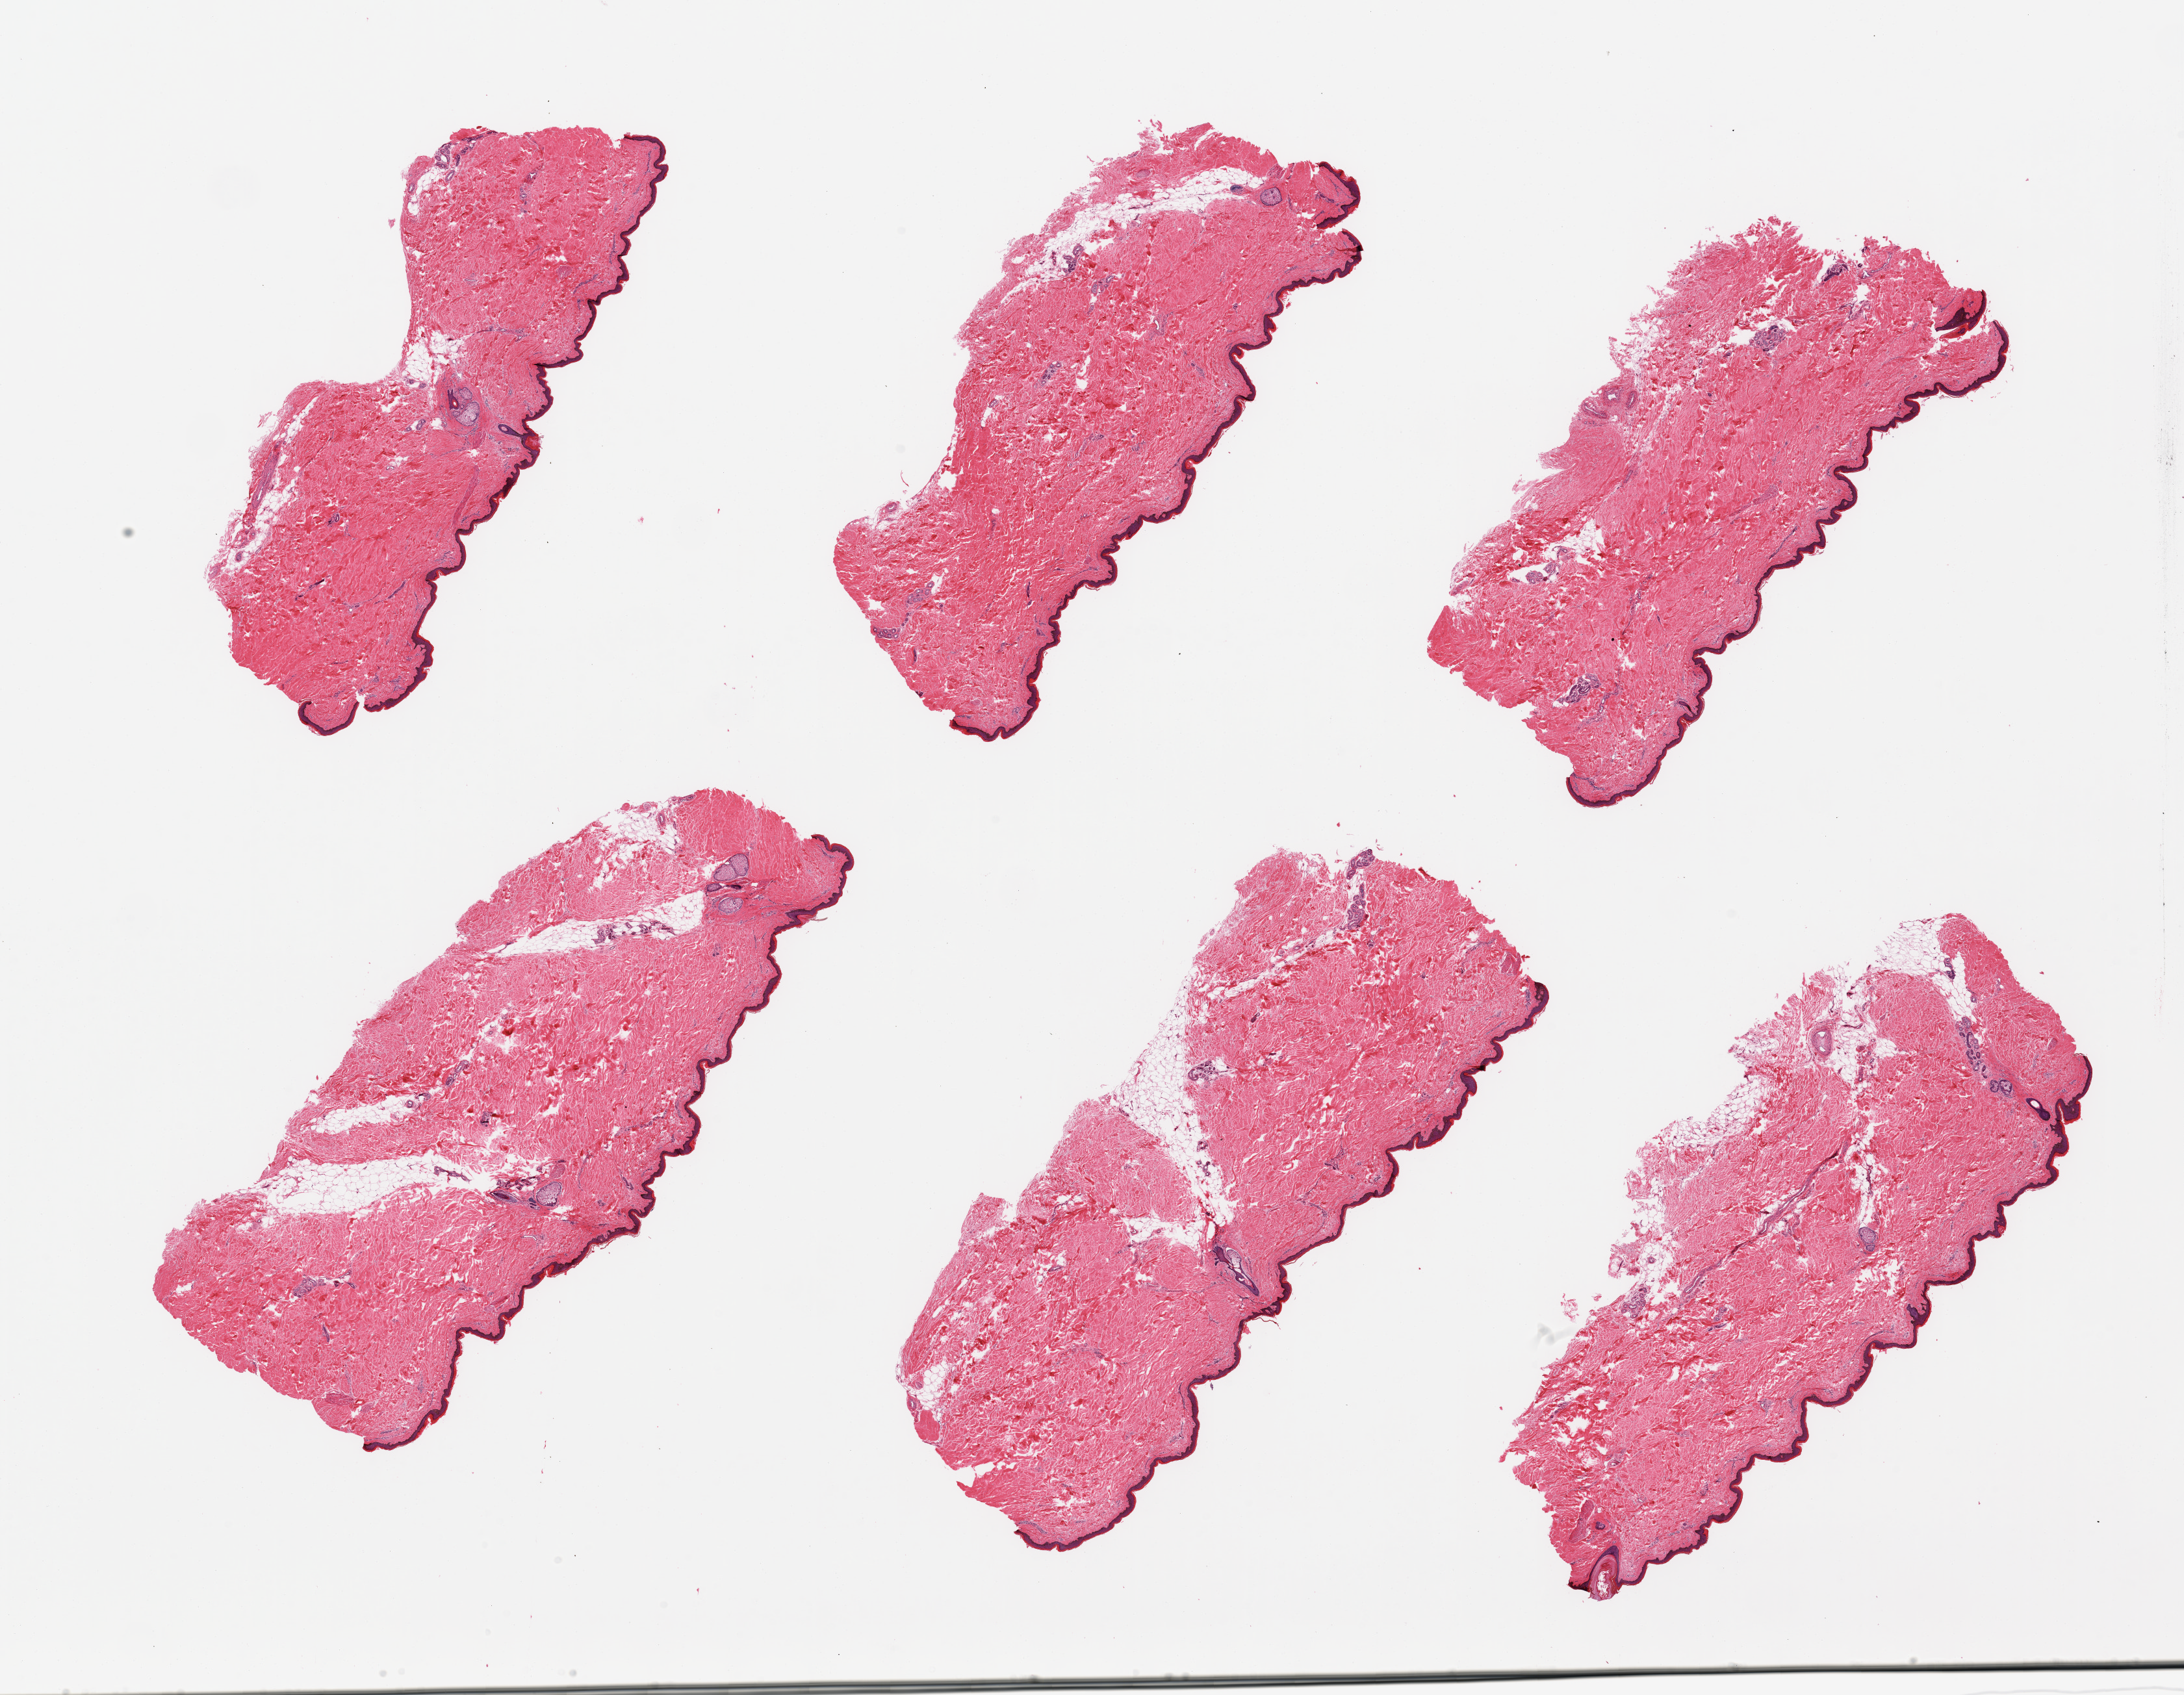
Digitized haematoxylin and eosin-stained section — shown as a low-resolution overview of the whole scanned area (about 26.6 x 20.6 mm); PAXgene-fixed, paraffin-embedded tissue; target tissue: skin of lower leg; donor tissue sample. Donor sex: male.
Review note (as recorded): 6 pieces; essentially well trimmed, but with up to 10% periadnexal fat, epidermis measures 34 microns.